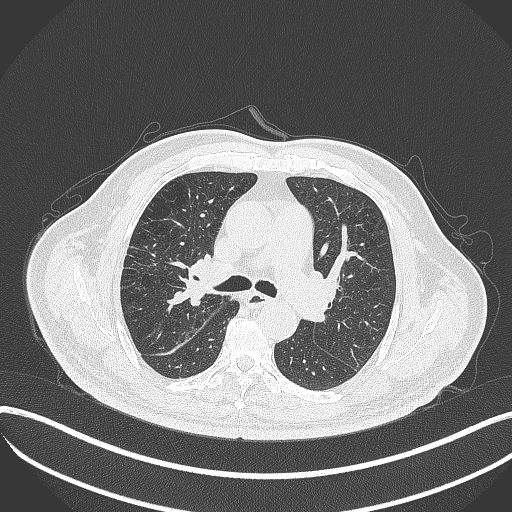
Chest CT, one axial slice. Slice 229 of 401 in the series (ordered by position). Reconstruction kernel B70f. 120 kVp. Lung window (W 1500 / L -600 HU). 512 × 512 image matrix, field of view 400 × 400 mm. Patient: male, 72 years. Case-level facts recorded for this patient, not image findings: clinical TNM (as recorded): T1c N0 M0; histopathological grade: G2.
Annotated regions visible in this slice (rectangle marked by the reading radiologist):
- lung tumour (recorded histology: squamous cell carcinoma): bounding box (x1, y1, x2, y2) in pixels: (174, 258, 210, 313)